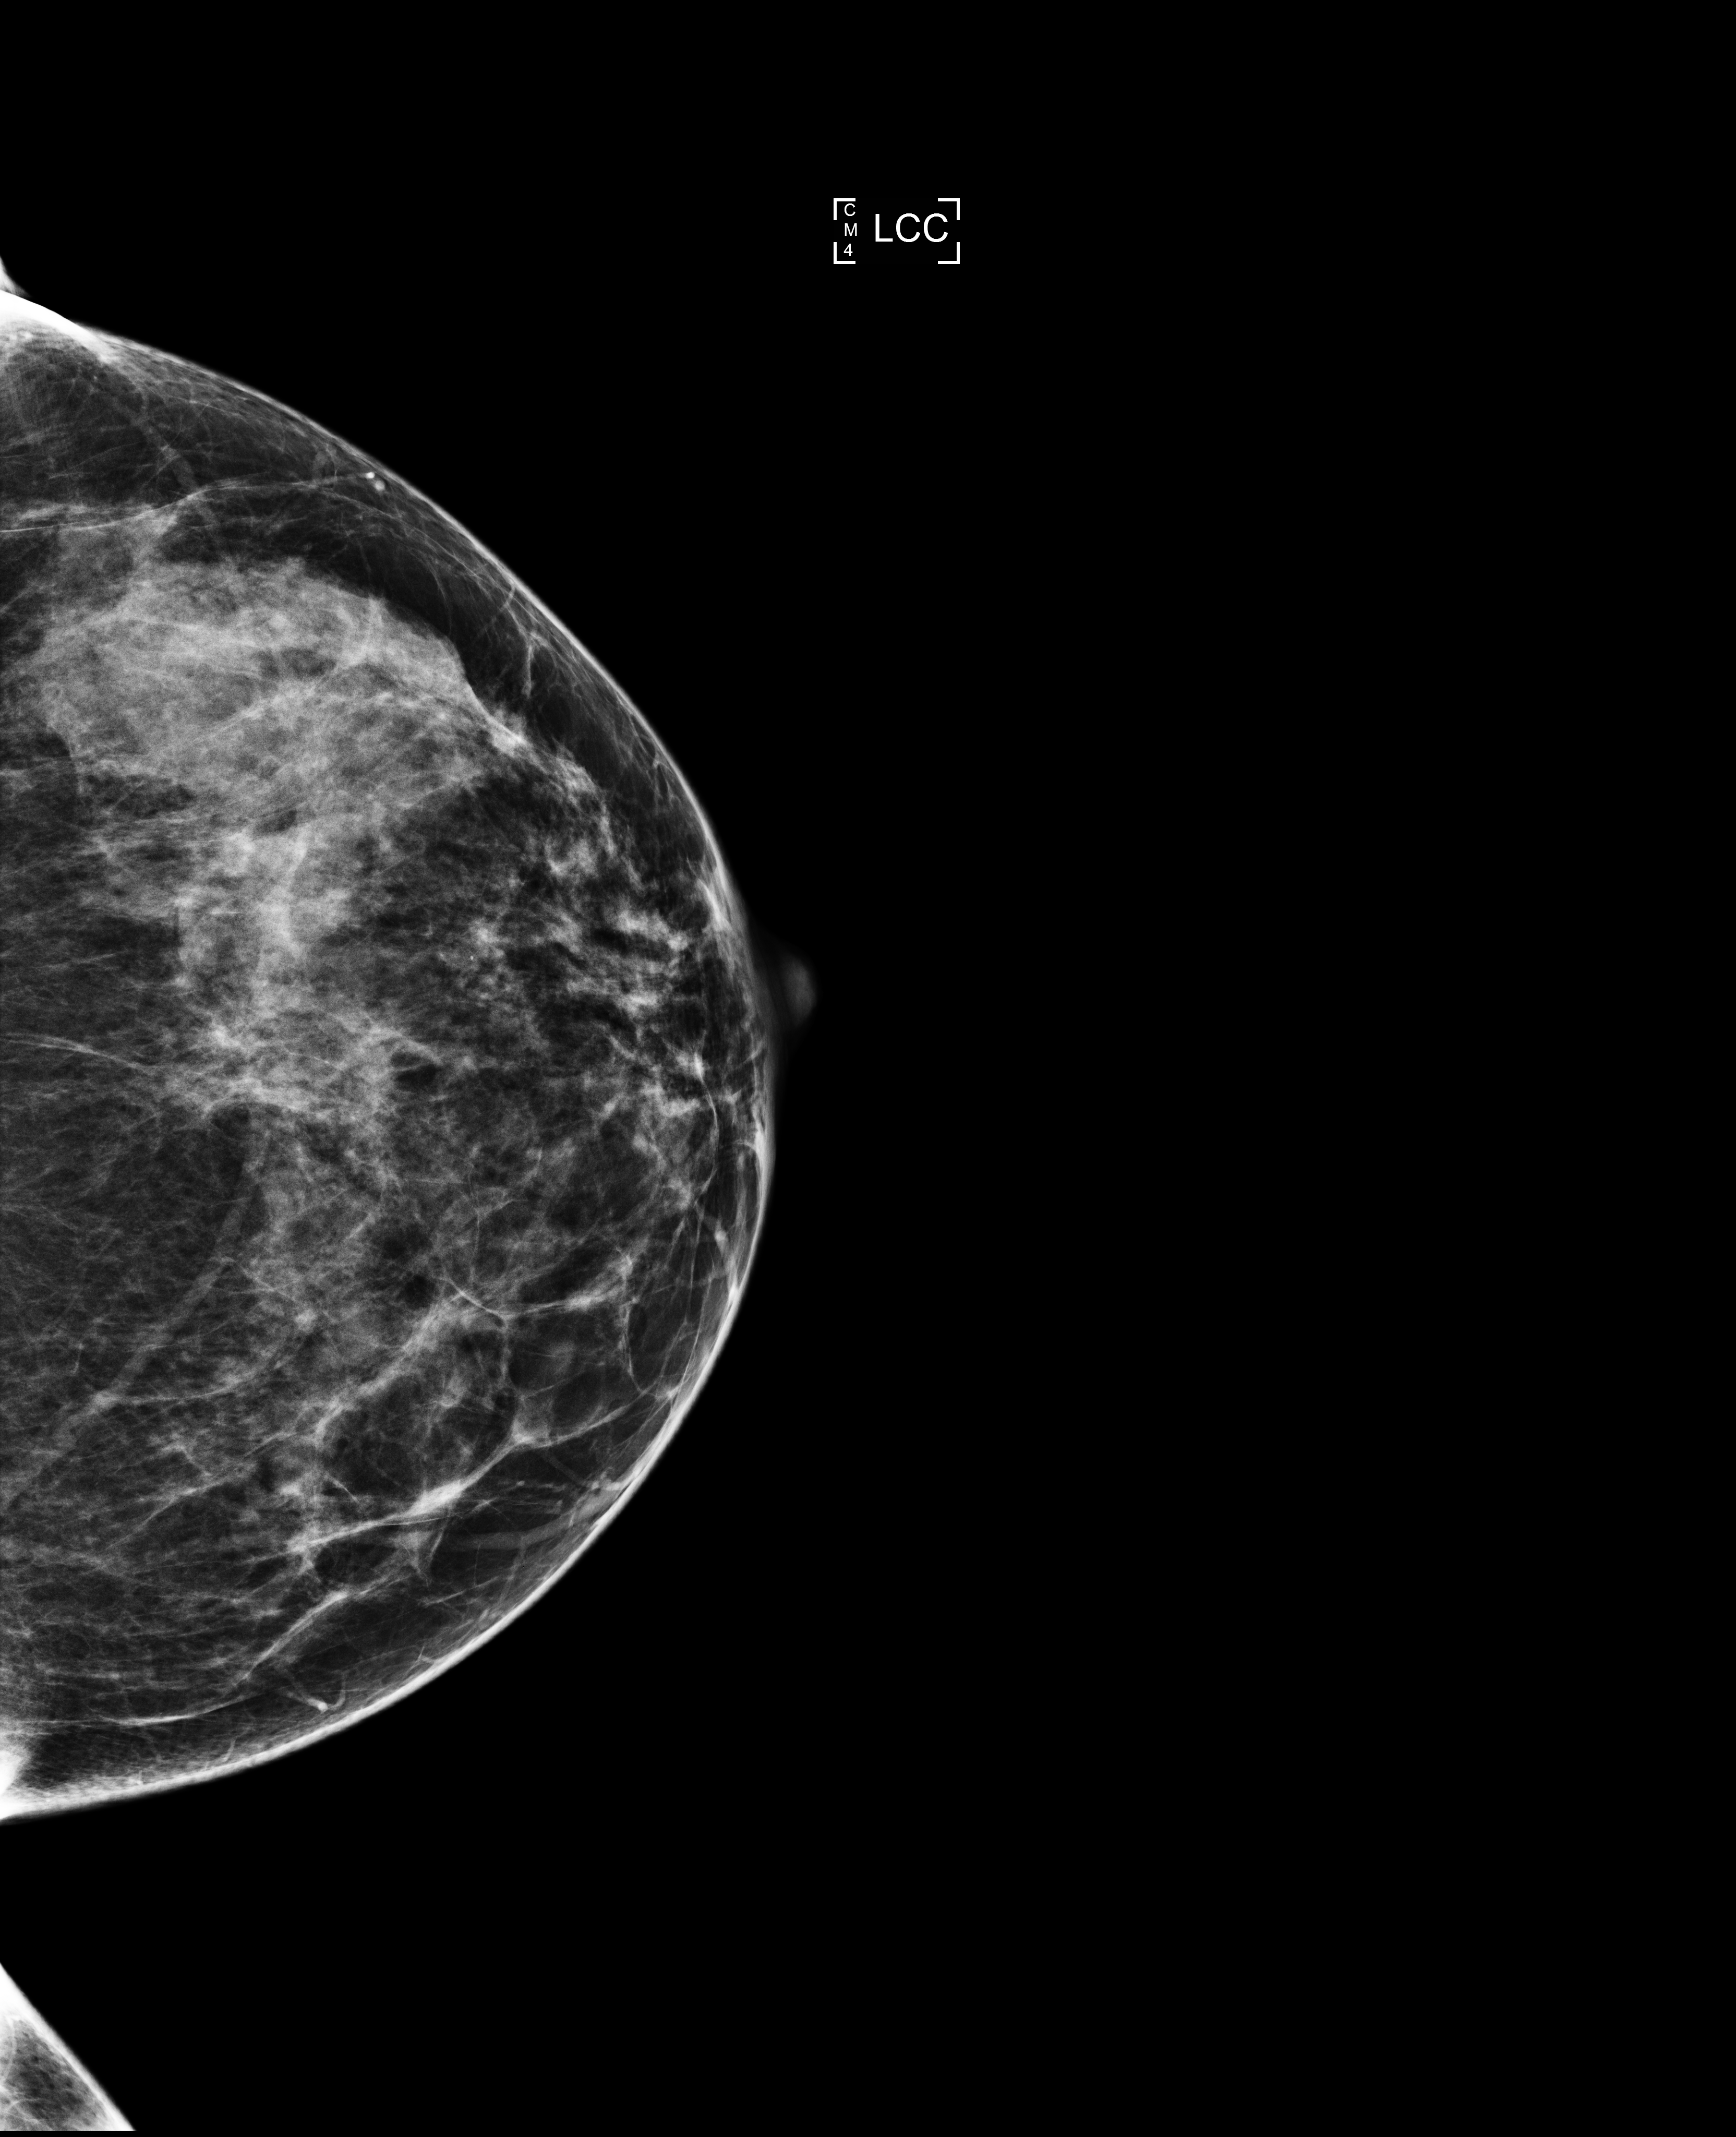
Full-field digital mammogram (FFDM); left breast; CC view; annual screening mammography examination; system: Selenia Dimensions. Patient: female, 46 years.
Breast density at the screening exam (both breasts): heterogeneously dense (BI-RADS density category c). Final BI-RADS category for the screening round (tomosynthesis exam, both breasts): category 1. Recall: no recall after this screen.